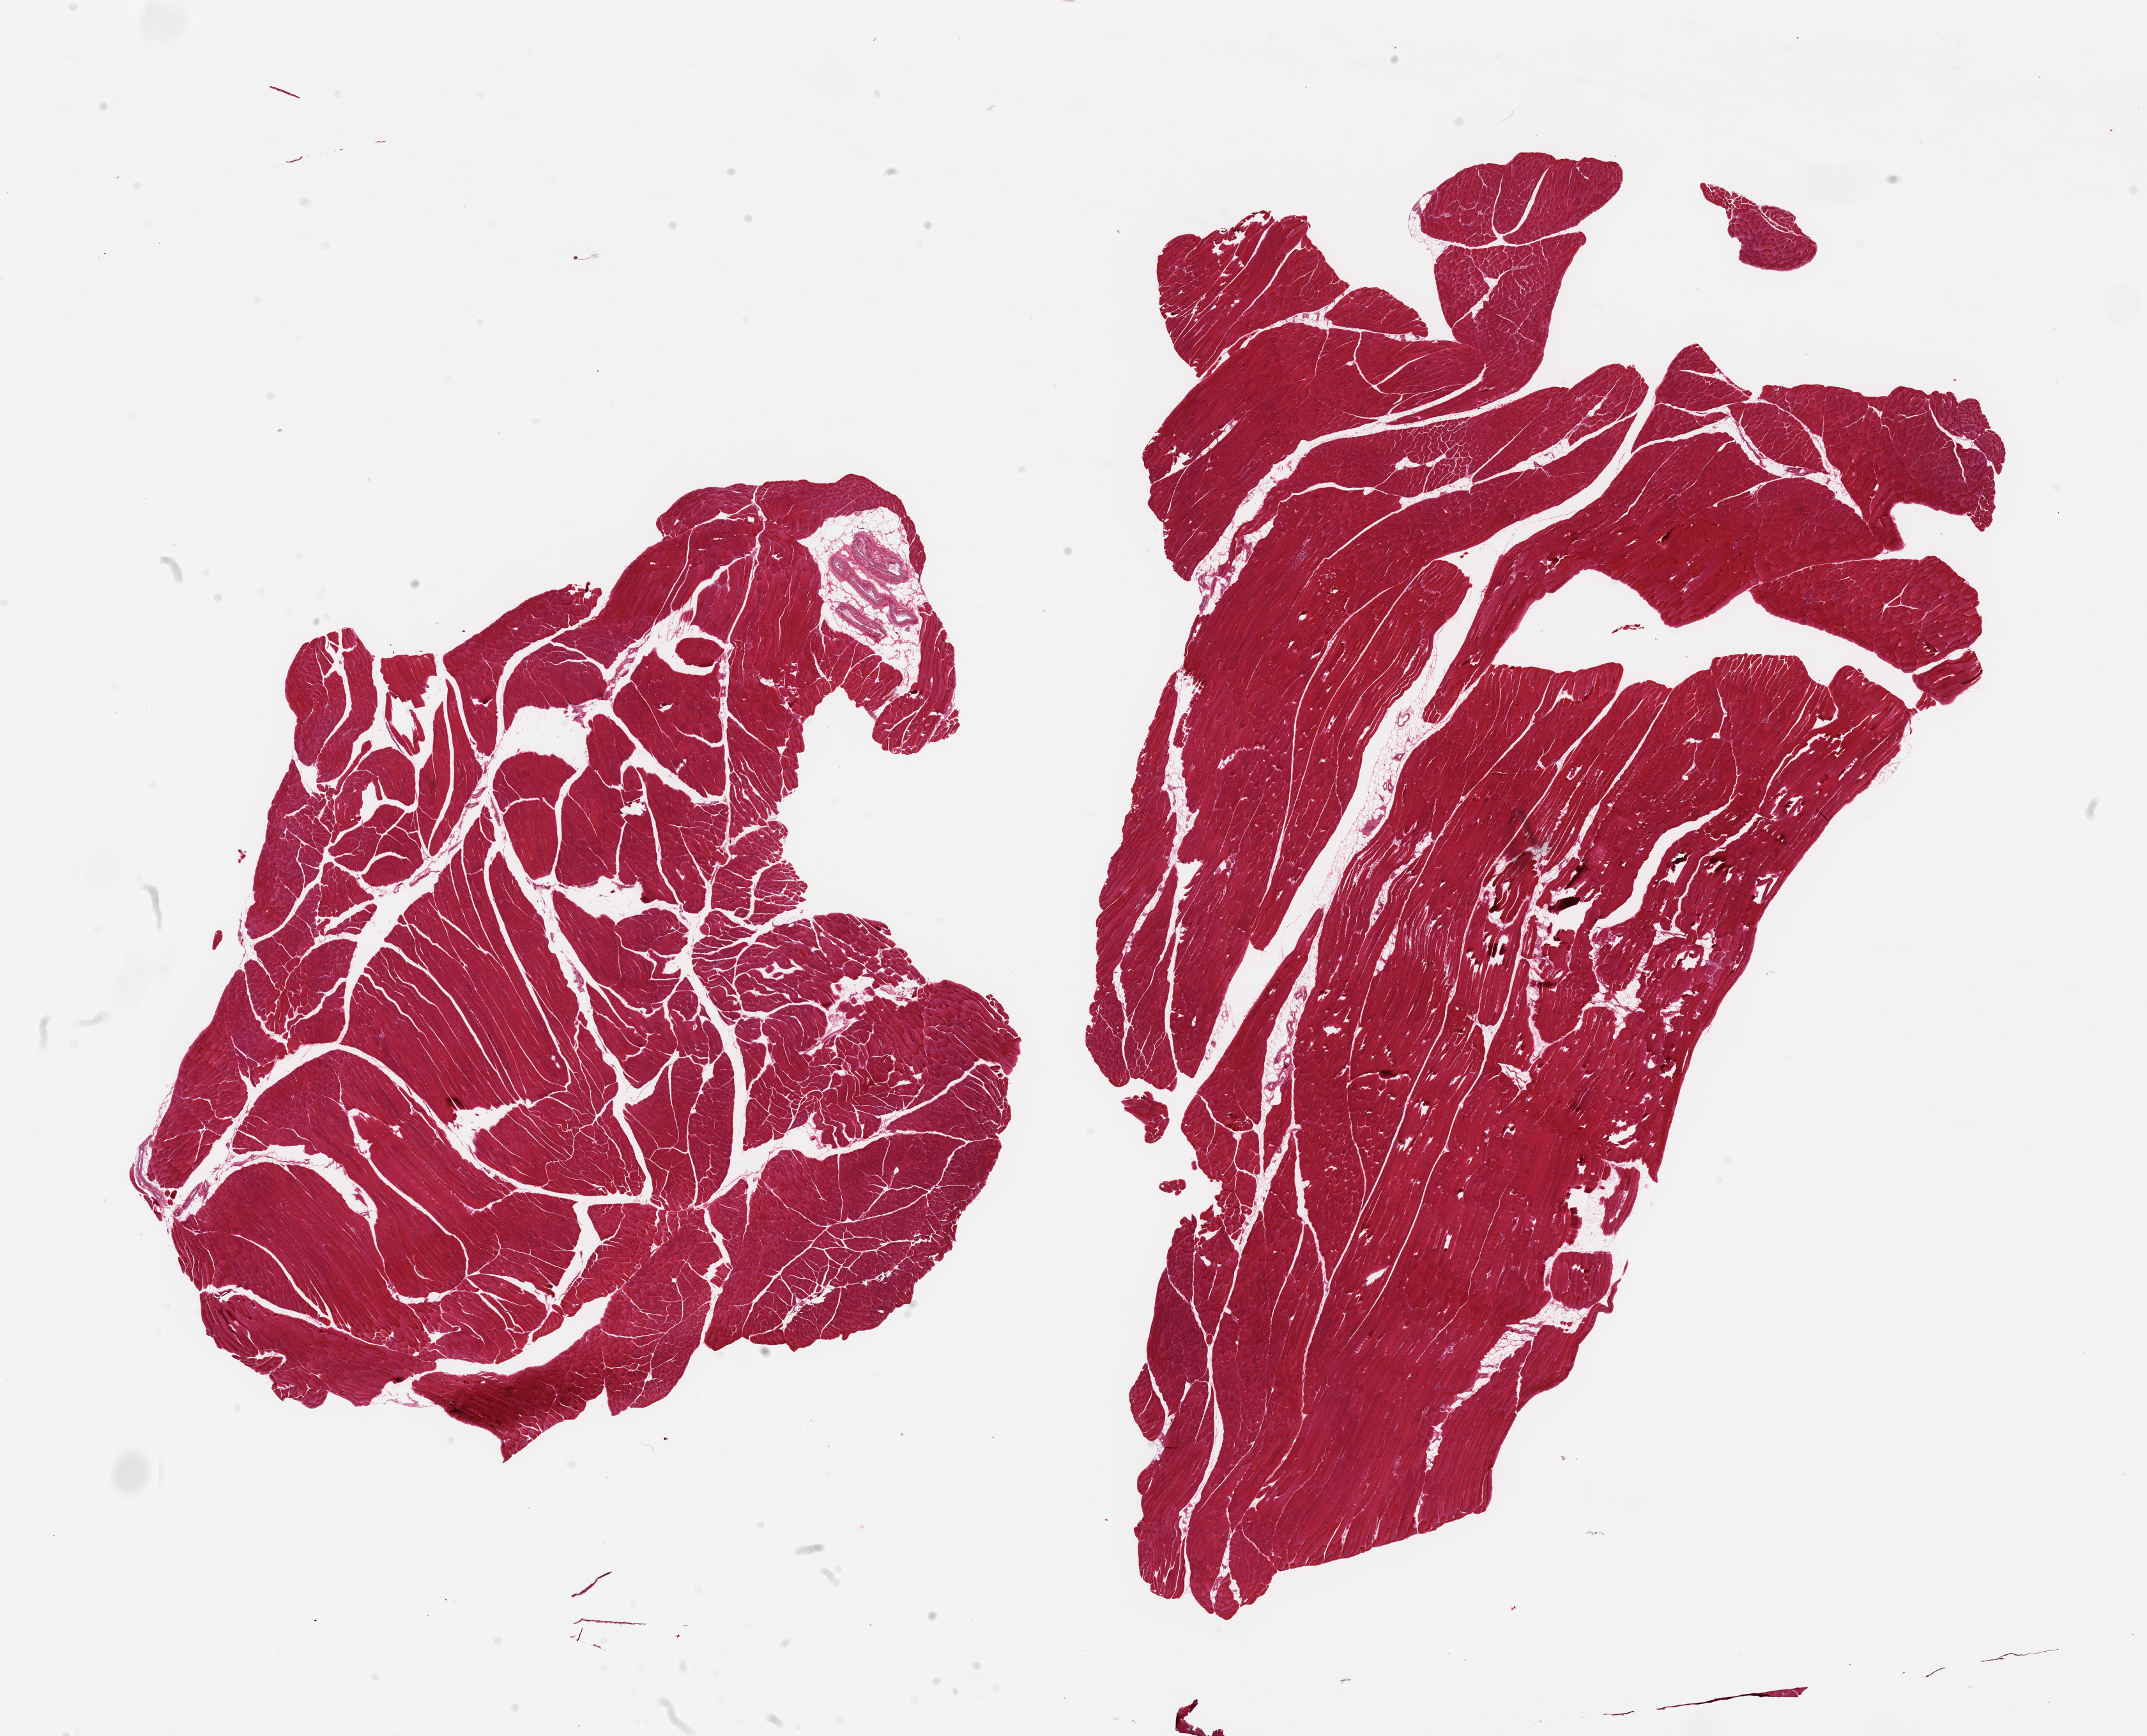
Whole-slide image, H&E stain — low-resolution overview of the scanned area, about 26.6 x 21.5 mm. PAXgene-fixed paraffin-embedded (PFPE) section. Target tissue: skeletal muscle. Tissue donor sample.
Review note (as recorded): 2 pieces, ~5-10% interstitial fat.